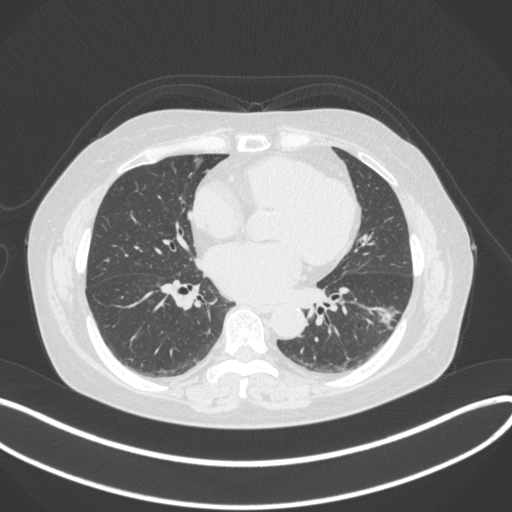
Chest CT, one axial slice. Position 158 of 373 along the scan axis. Reconstruction kernel B31f. 120 kVp. Lung window (W 1500 / L -600 HU). 1 mm slice thickness. 512 × 512 image matrix, field of view 400 × 400 mm. Female patient, age 67 years. Case-level facts recorded for this patient, not image findings: clinical TNM (as recorded): T1c N0 M0; histopathological grade: G2.
Structures marked on this image (bounding box drawn by a radiologist):
- lung tumour (recorded histology: adenocarcinoma): bounding box <367,302,402,329> (left, top, right, bottom; pixels)